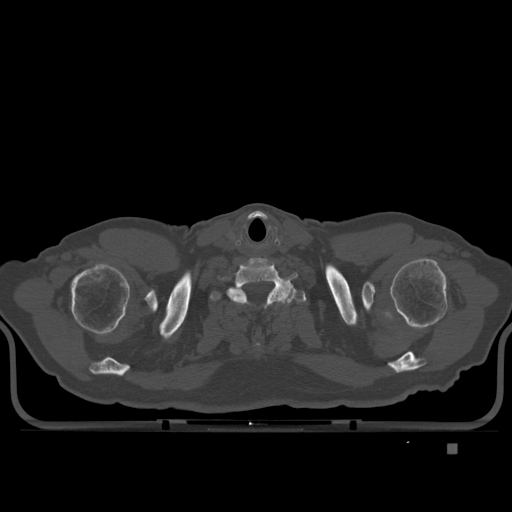
CT including the spine, one axial slice; slice 331 of 435 in the series (ordered by position); bone window (W 1800 / L 400 HU); 1.5 mm slice thickness; 512 × 512 image matrix, field of view 434 × 434 mm. Male patient, age 73 years. Case-level facts recorded for this patient, not image findings: primary cancer: skin.
Outlined on this slice (semi-automatic segmentation, software-assisted and operator-edited):
- T1 vertebra: box from (x=211, y=283) to (x=304, y=346) px